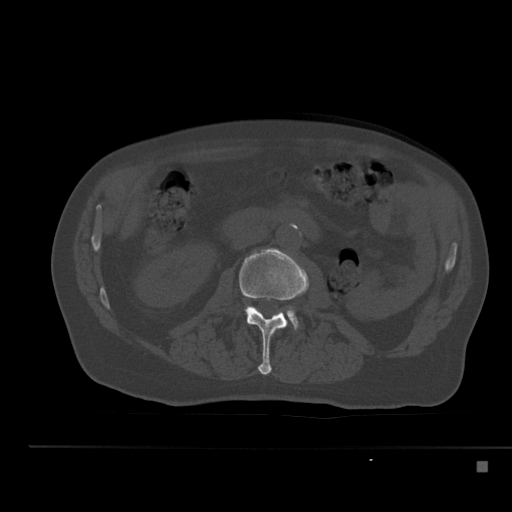
CT including the spine, one axial slice. Slice 181 of 517 in the series (ordered by position). 120 kVp. Bone window (W 1800 / L 400 HU). 1.5 mm slice thickness. 512 × 512 image matrix, field of view 408 × 408 mm. Patient: male, 70 years. Case-level facts recorded for this patient, not image findings: primary cancer: renal; vertebrae with lytic lesions (as recorded): T4, T6, T10, T12, L3, L4, L5.
Structures marked on this image (semi-automatic segmentation, software-assisted and operator-edited):
- L2 vertebra: bounding box [x1, y1, x2, y2] px = [239, 248, 309, 375]
- L3 vertebra: [286, 309, 298, 329]